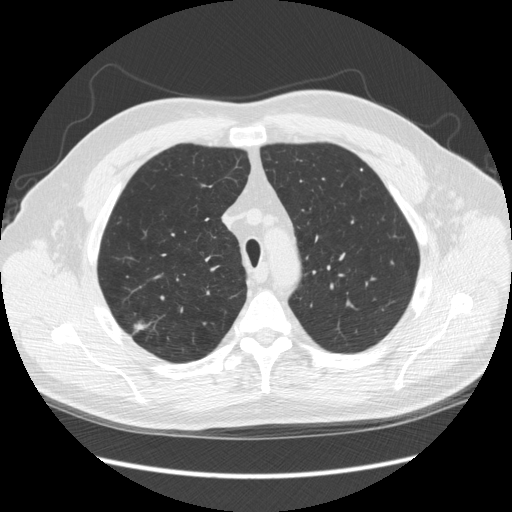
Low-dose screening chest CT, axial slice, third screening round (two years after baseline), lung window (W 1500 / L -600 HU), 2.5 mm slice thickness, standard (soft-tissue) reconstruction kernel (STANDARD), slice 56 of 248 in the series, 512 × 512 image matrix, field of view 380 × 380 mm. Male, age 64 years at enrolment.
Lesion marked by an expert reader, bounding box (x1, y1, x2, y2) in pixels: (119, 313, 168, 354). The screening reader recorded 4 non-calcified nodules or masses ≥4 mm on this exam (right upper lobe, right upper lobe, right upper lobe, right upper lobe); which of them this box marks is not recorded. Later outcome: lung cancer diagnosed 15 days after this screen — adenocarcinoma, NOS, right upper lobe, moderately differentiated (G2), stage IA (AJCC 6th edition), 14 mm at pathology.